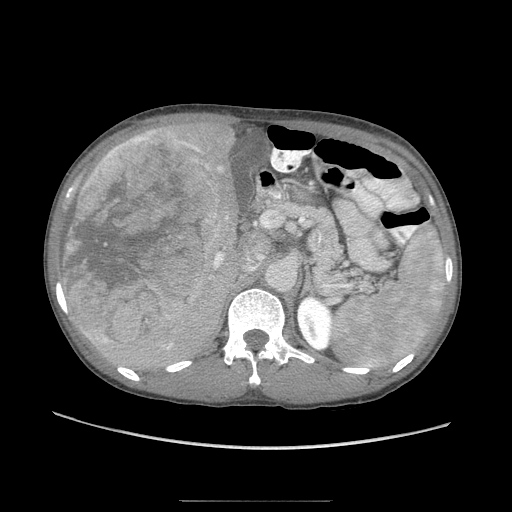
Contrast-enhanced abdominal CT (liver protocol), one axial slice; slice 50 of 103 in the series (ordered by position); reconstruction kernel STANDARD; soft-tissue window (W 400 / L 40 HU); 2.5 mm slice thickness; 512 × 512 image matrix, field of view 380 × 380 mm. From the clinical record (not read from this slice): diagnosis: hepatocellular carcinoma (patient treated with transarterial chemoembolisation; whether this scan precedes or follows treatment is not stated here); TNM stage (as recorded): Stage-IIIA; Child-Pugh class: A; tumour nodularity: multinodular.
Structures marked on this image (semi-automatically segmented with operator editing):
- liver parenchyma outside the tumour (the mass and vessels are separate outlines, so this box may not span the whole liver): bounding box <66,116,254,382> (left, top, right, bottom; pixels)
- mass: <61,127,219,346>
- liver vessels: <188,142,222,278>